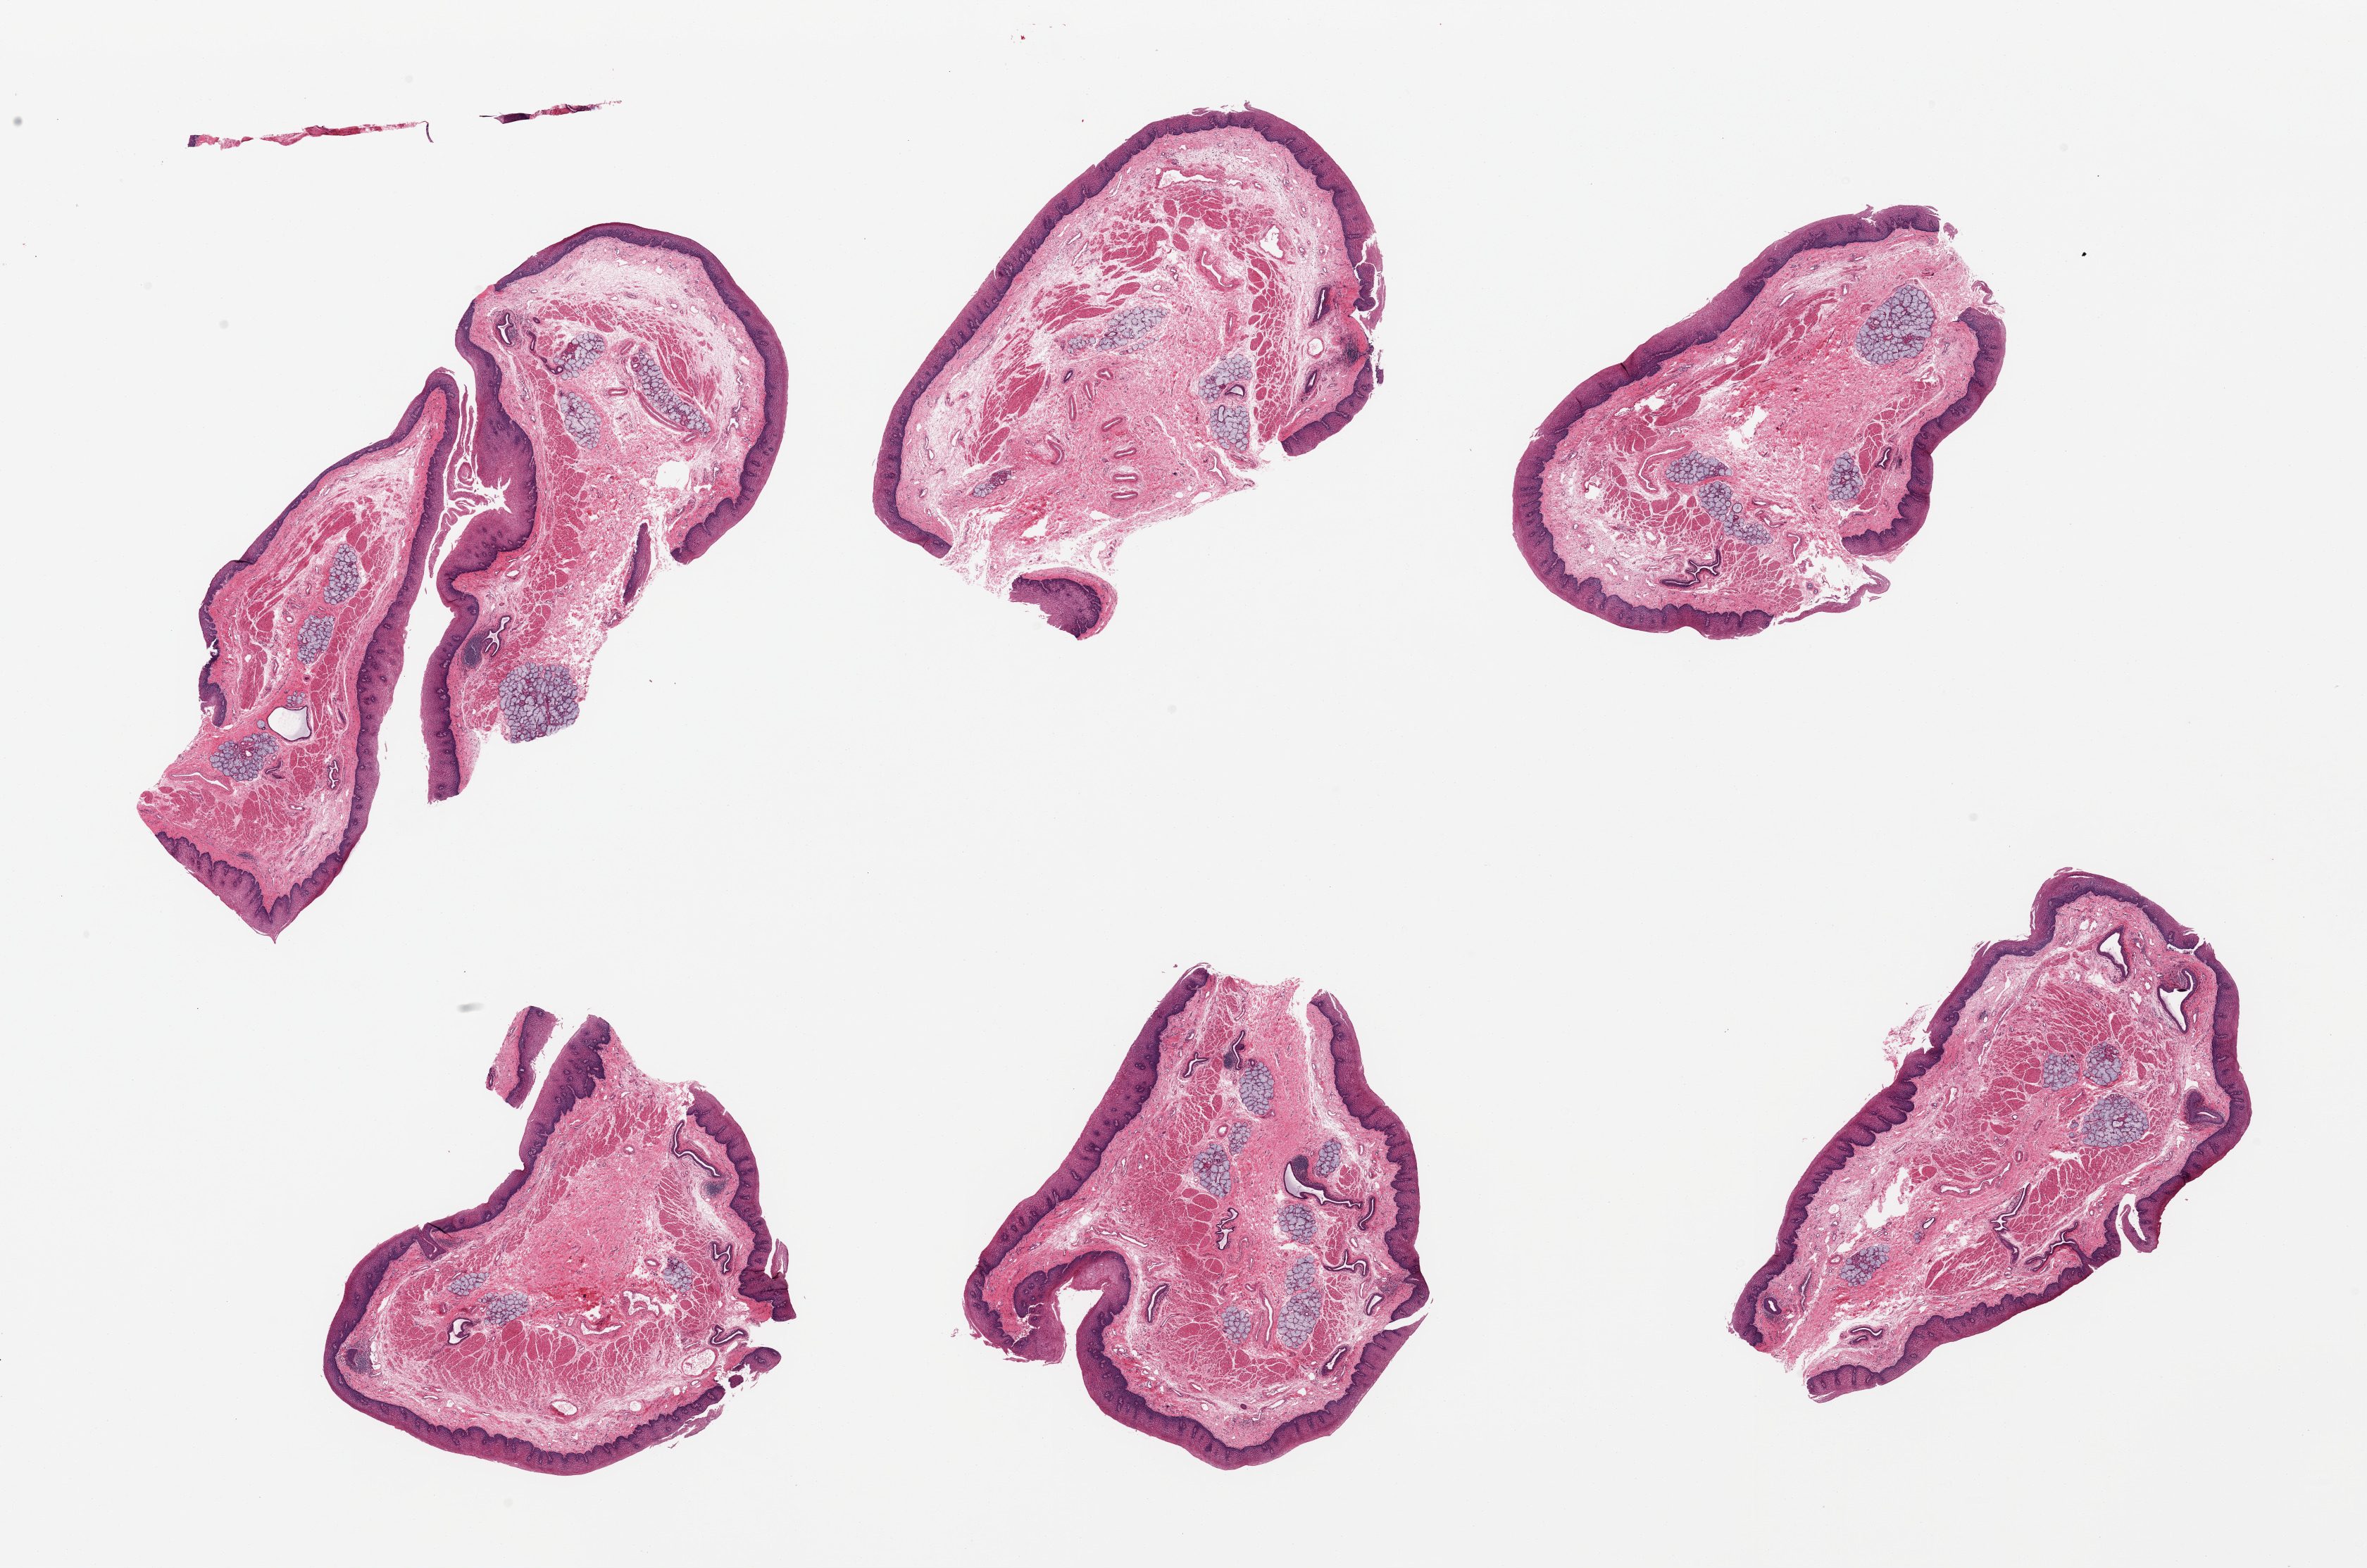
Haematoxylin and eosin whole-slide image, brightfield, low-resolution overview of the scanned area, about 26.6 x 17.6 mm, PAXgene-fixed, paraffin-embedded tissue, section of gastroesophageal junction (target tissue), donor tissue sample. Male donor.
Pathologist's review note for this sample: 6 pieces; all contain esophageal squamous mucosa, not muscularis propria [target].